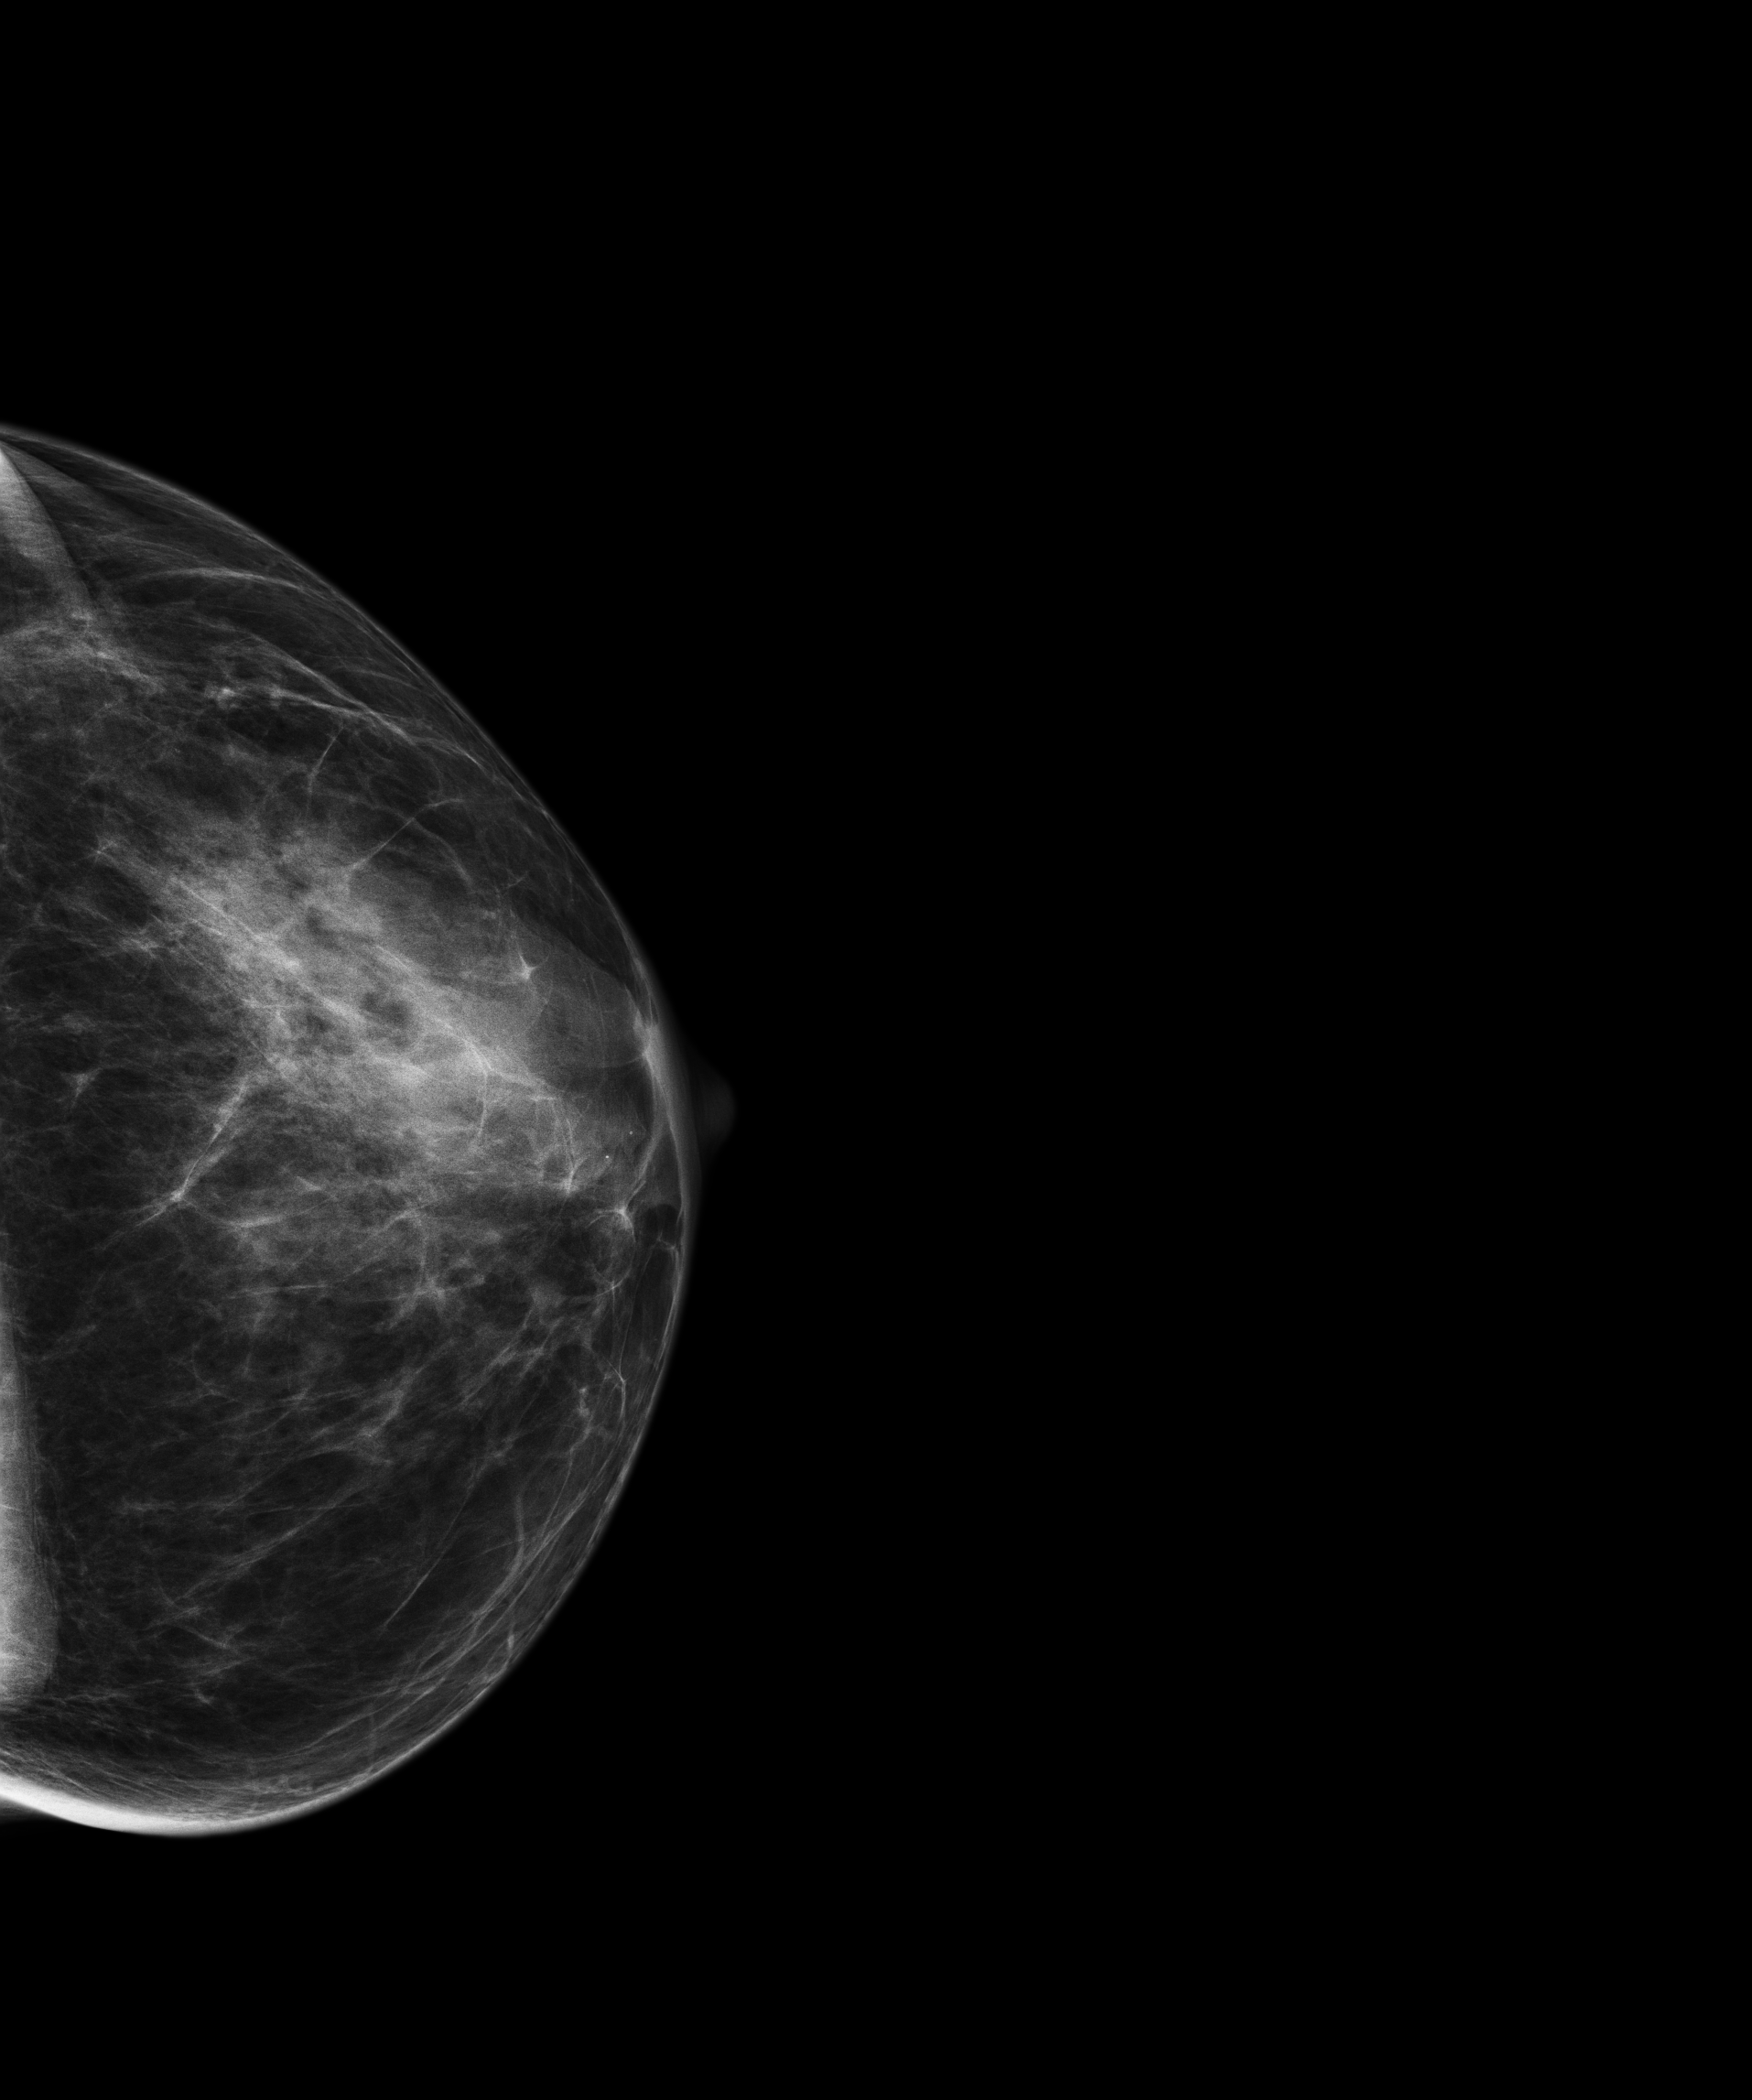
Digital mammogram (FFDM); left breast; craniocaudal (CC) view; annual screening mammography examination; compressed breast thickness 41 mm; system: Senographe Essential ADS_56.21.3. Patient aged 65 years (female).
BI-RADS breast density category at the screening exam (both breasts, scale 1–4): 3. Final BI-RADS assessment for this screening round (tomosynthesis exam, both breasts): category 1. Recall: no recall after this screen.